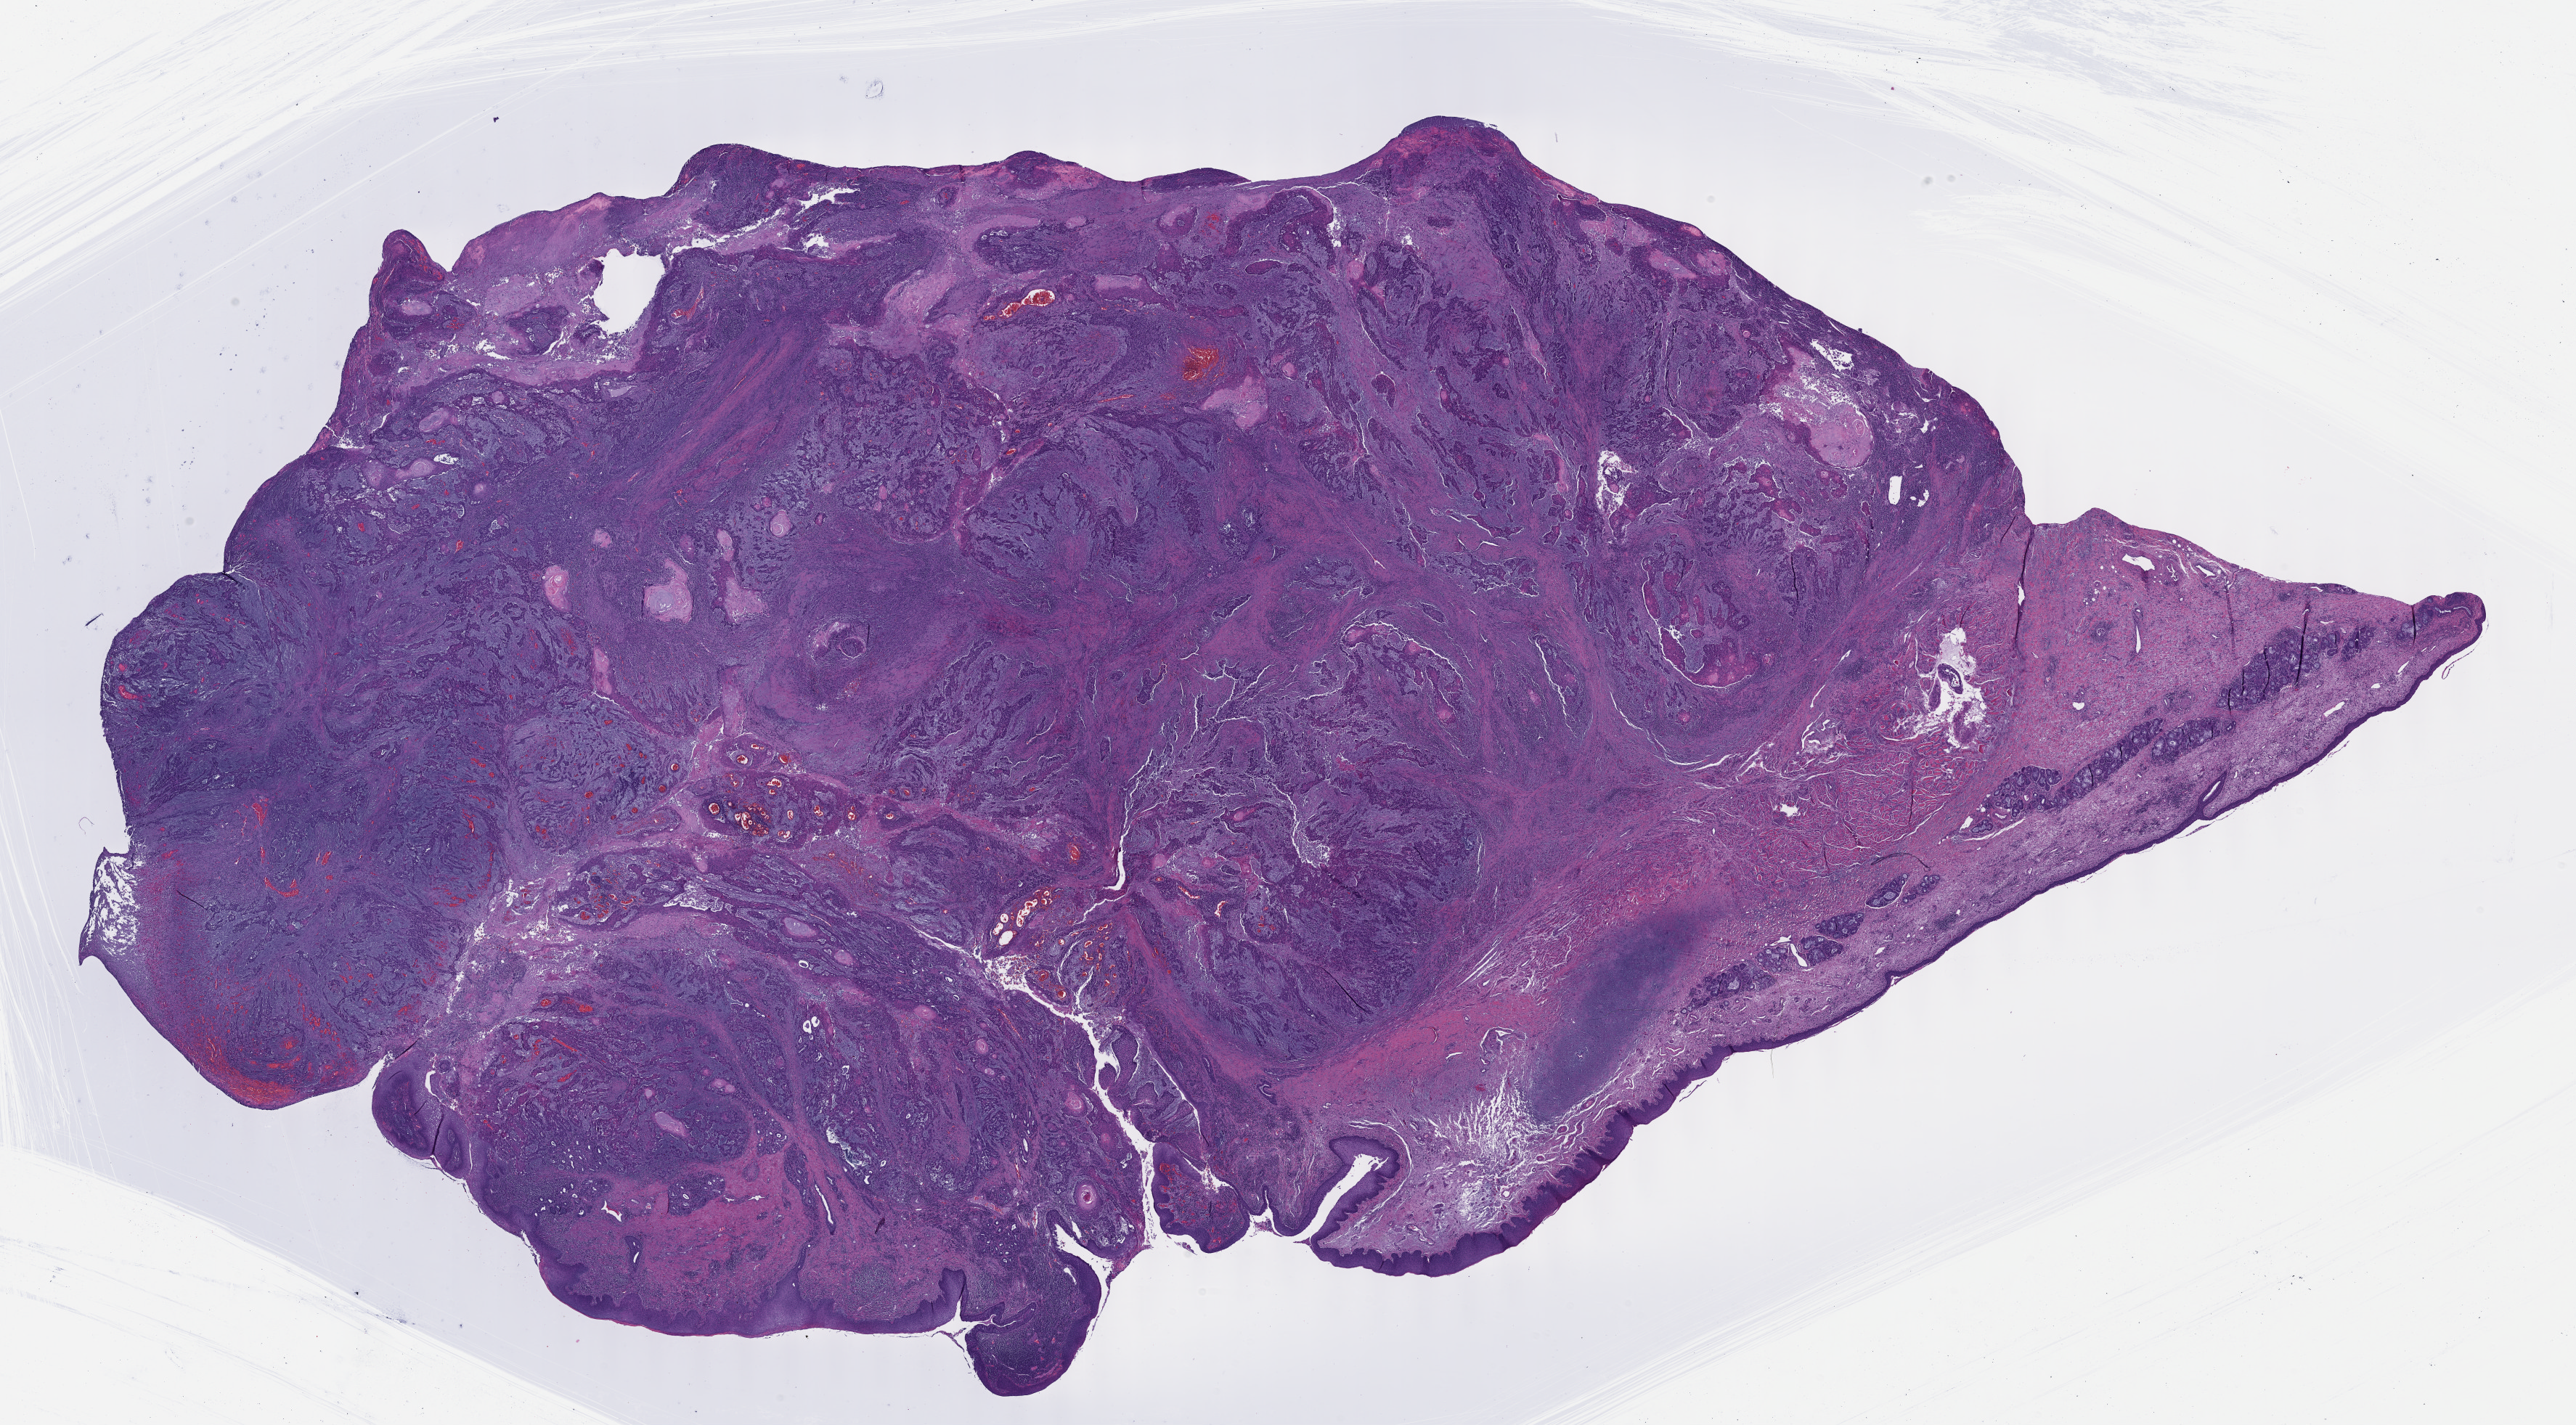
Digitized H&E-stained tissue section (whole slide) — shown as a low-resolution overview of the whole scanned area (about 28.7 x 15.9 mm, slide scanned at 40x); formalin-fixed paraffin-embedded (FFPE) diagnostic section; primary tumour sample from the head and neck. Patient: male, age at initial diagnosis 58 years. Histologic grade: G3 (poorly differentiated).
AJCC pathologic stage: IVA. Pathologic diagnosis: Squamous cell carcinoma, NOS (larynx, NOS).